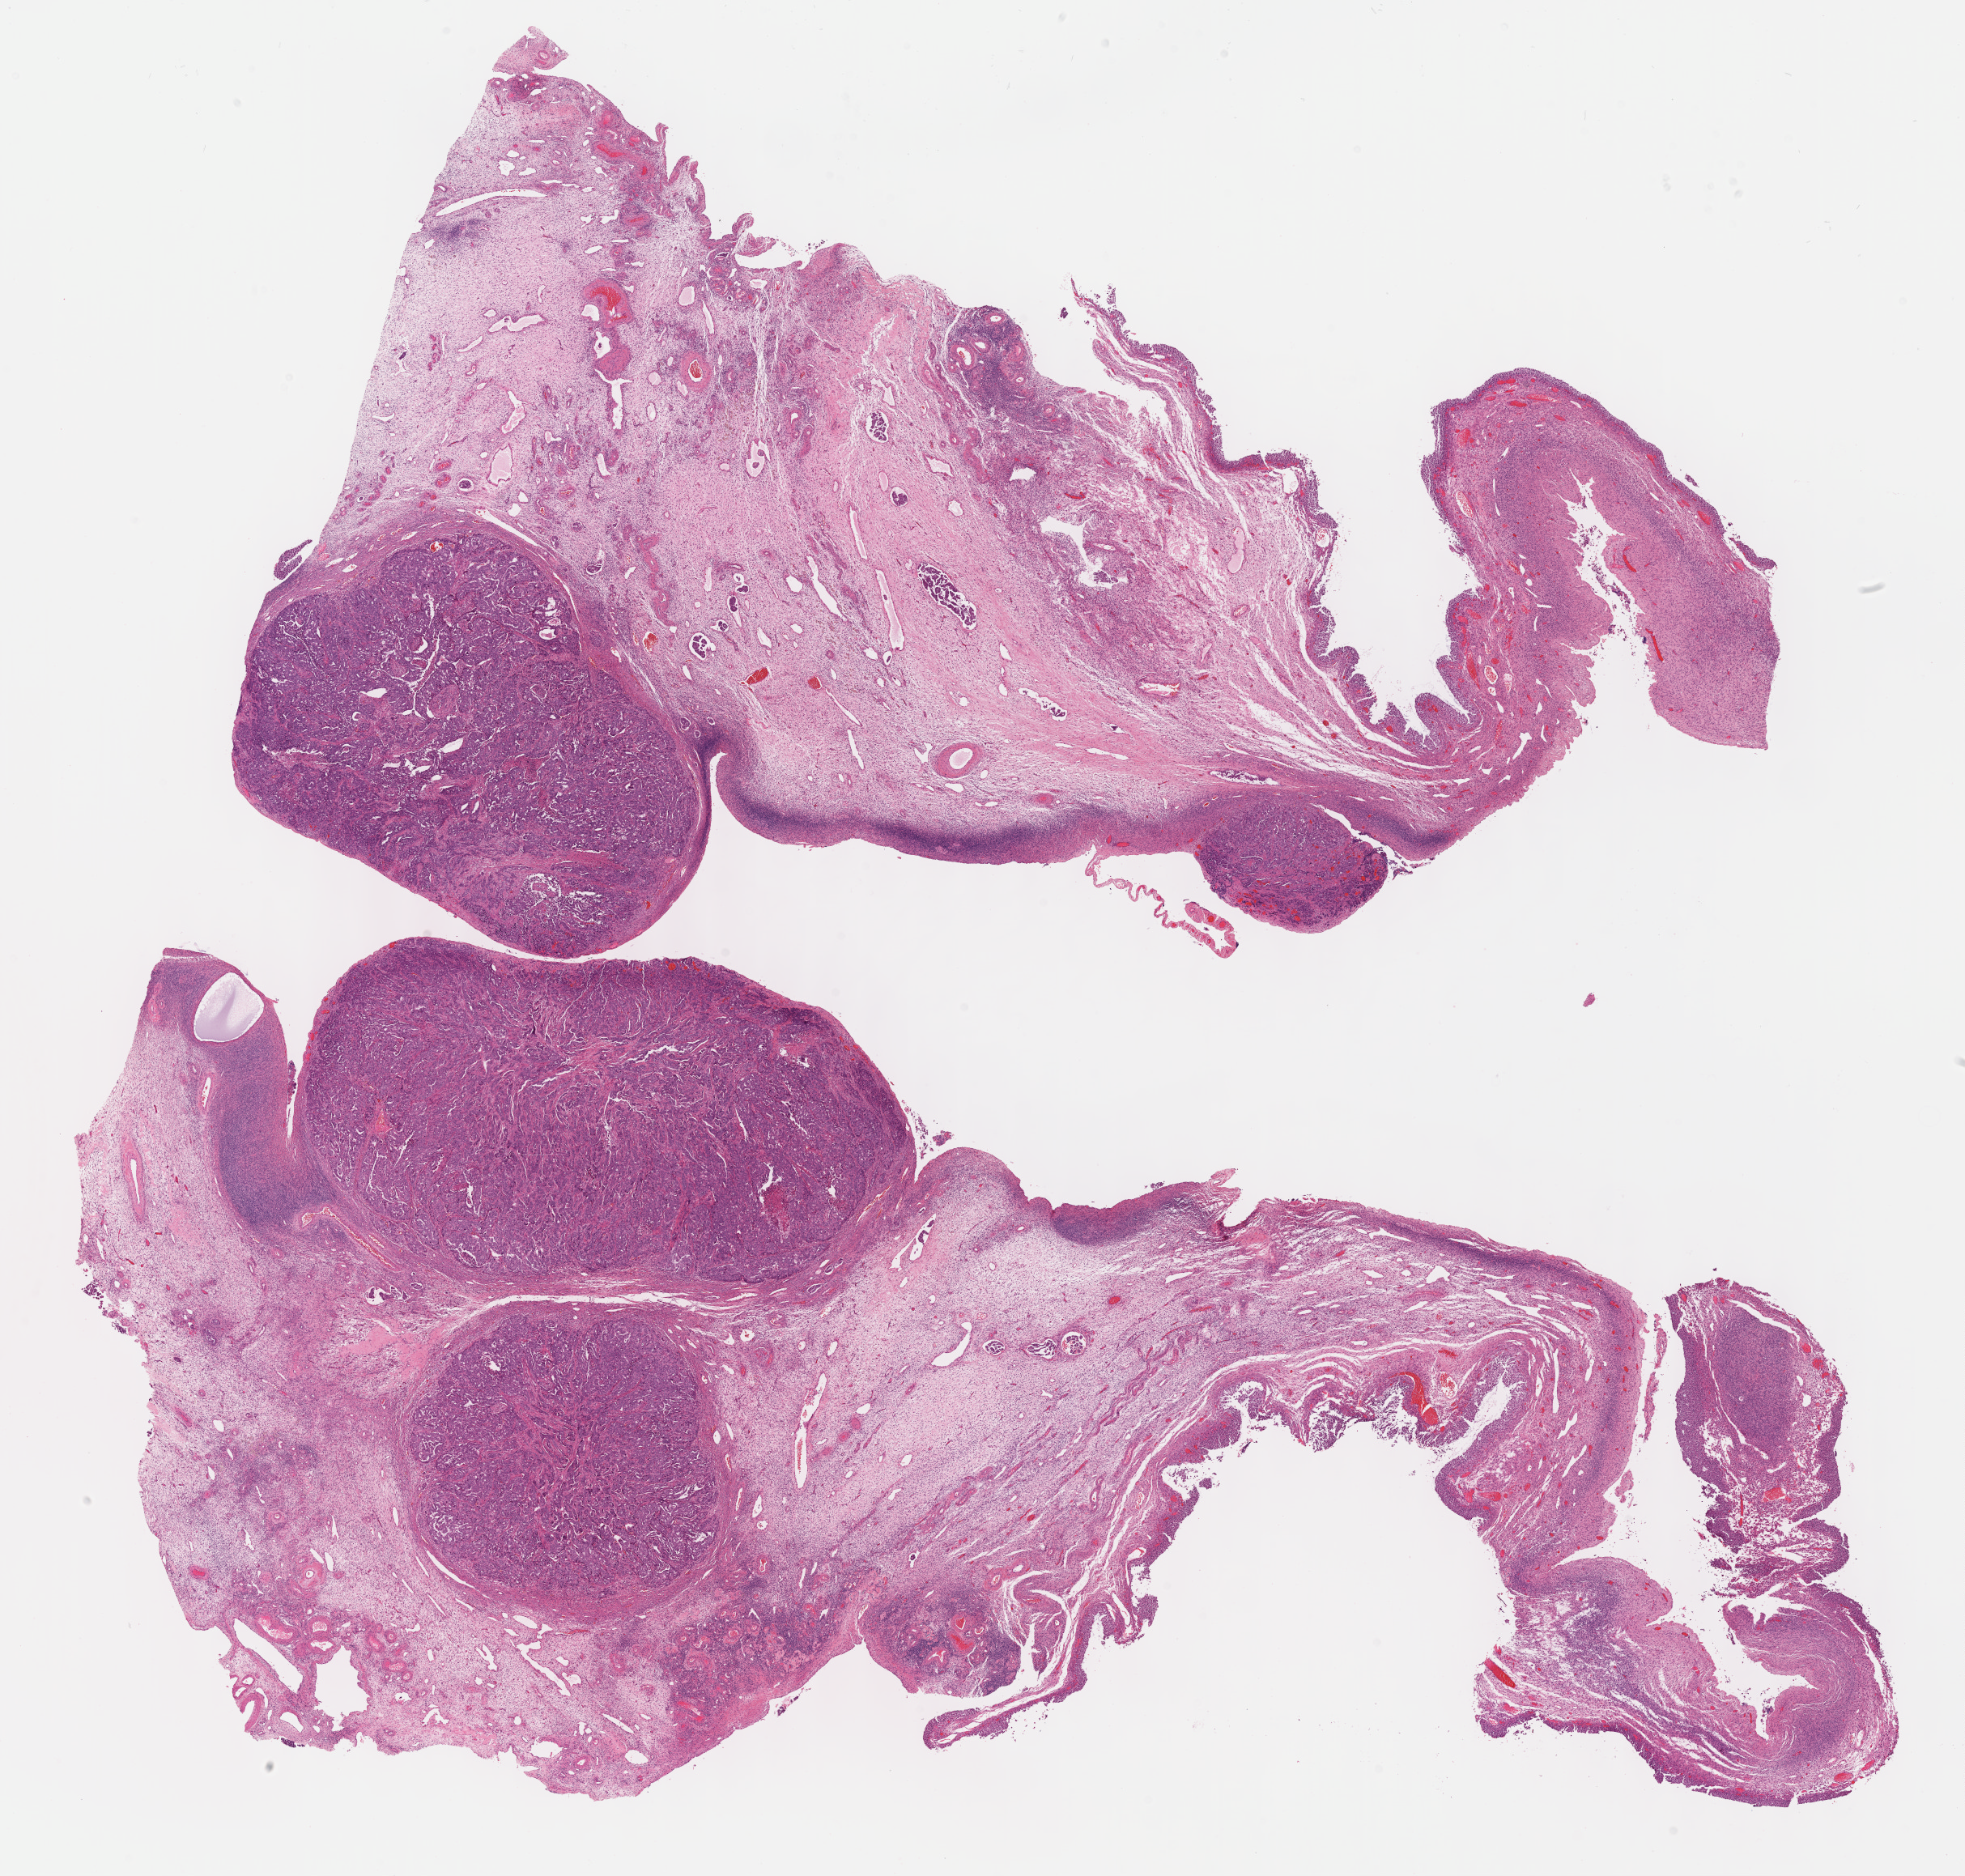
Digitized Hematoxylin and eosin (H&E) stained tissue section (whole slide) — whole scanned area (about 19.6 x 18.7 mm) shown as a low-resolution overview. Formalin-fixed paraffin-embedded (FFPE) diagnostic section. Ovary, primary tumour sample. Patient: female, age at initial diagnosis 45 years. Histologic grade: G3 (poorly differentiated).
Laterality: right. Diagnosis: Serous cystadenocarcinoma, NOS. FIGO stage: IV.